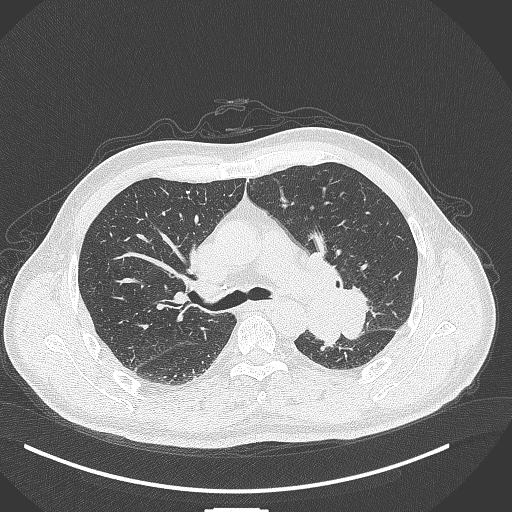
Chest CT, one axial slice; slice 270 of 429 in the series (ordered by position); reconstruction kernel B70f; lung window (W 1500 / L -600 HU); 1 mm slice thickness; 512 × 512 image matrix, field of view 400 × 400 mm. Male patient, age 55 years. Case-level facts recorded for this patient, not image findings: clinical TNM (as recorded): T3 N0 M1c; histopathological grade: G3.
Annotated regions visible in this slice (bounding box drawn by a radiologist):
- lung tumour (recorded histology: adenocarcinoma): bounding box [x1, y1, x2, y2] px = [312, 248, 373, 350]